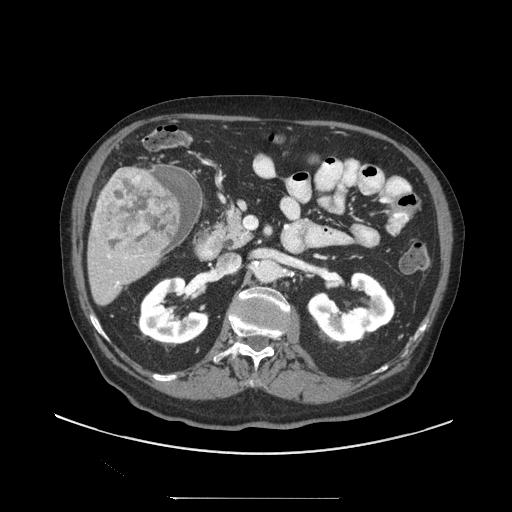
Contrast-enhanced abdominal CT (liver protocol), one axial slice; slice 41 of 97 in the series (ordered by position); reconstruction kernel STANDARD; 140 kVp; soft-tissue window (W 400 / L 40 HU); 2.5 mm slice thickness; 512 × 512 image matrix, field of view 450 × 450 mm. Case-level facts recorded for this patient, not image findings: diagnosis: hepatocellular carcinoma (patient treated with transarterial chemoembolisation; whether this scan precedes or follows treatment is not stated here); TNM stage (as recorded): Stage-IIIC; Child-Pugh class: A; tumour nodularity: uninodular; tumour size: 9.2 cm.
Structures marked on this image (semi-automatic segmentation, software-assisted and operator-edited):
- liver parenchyma outside the tumour (the mass and vessels are separate outlines, so this box may not span the whole liver): bounding box [x1, y1, x2, y2] px = [86, 166, 182, 306]
- mass: [98, 169, 180, 256]
- liver vessels: [108, 255, 119, 287]